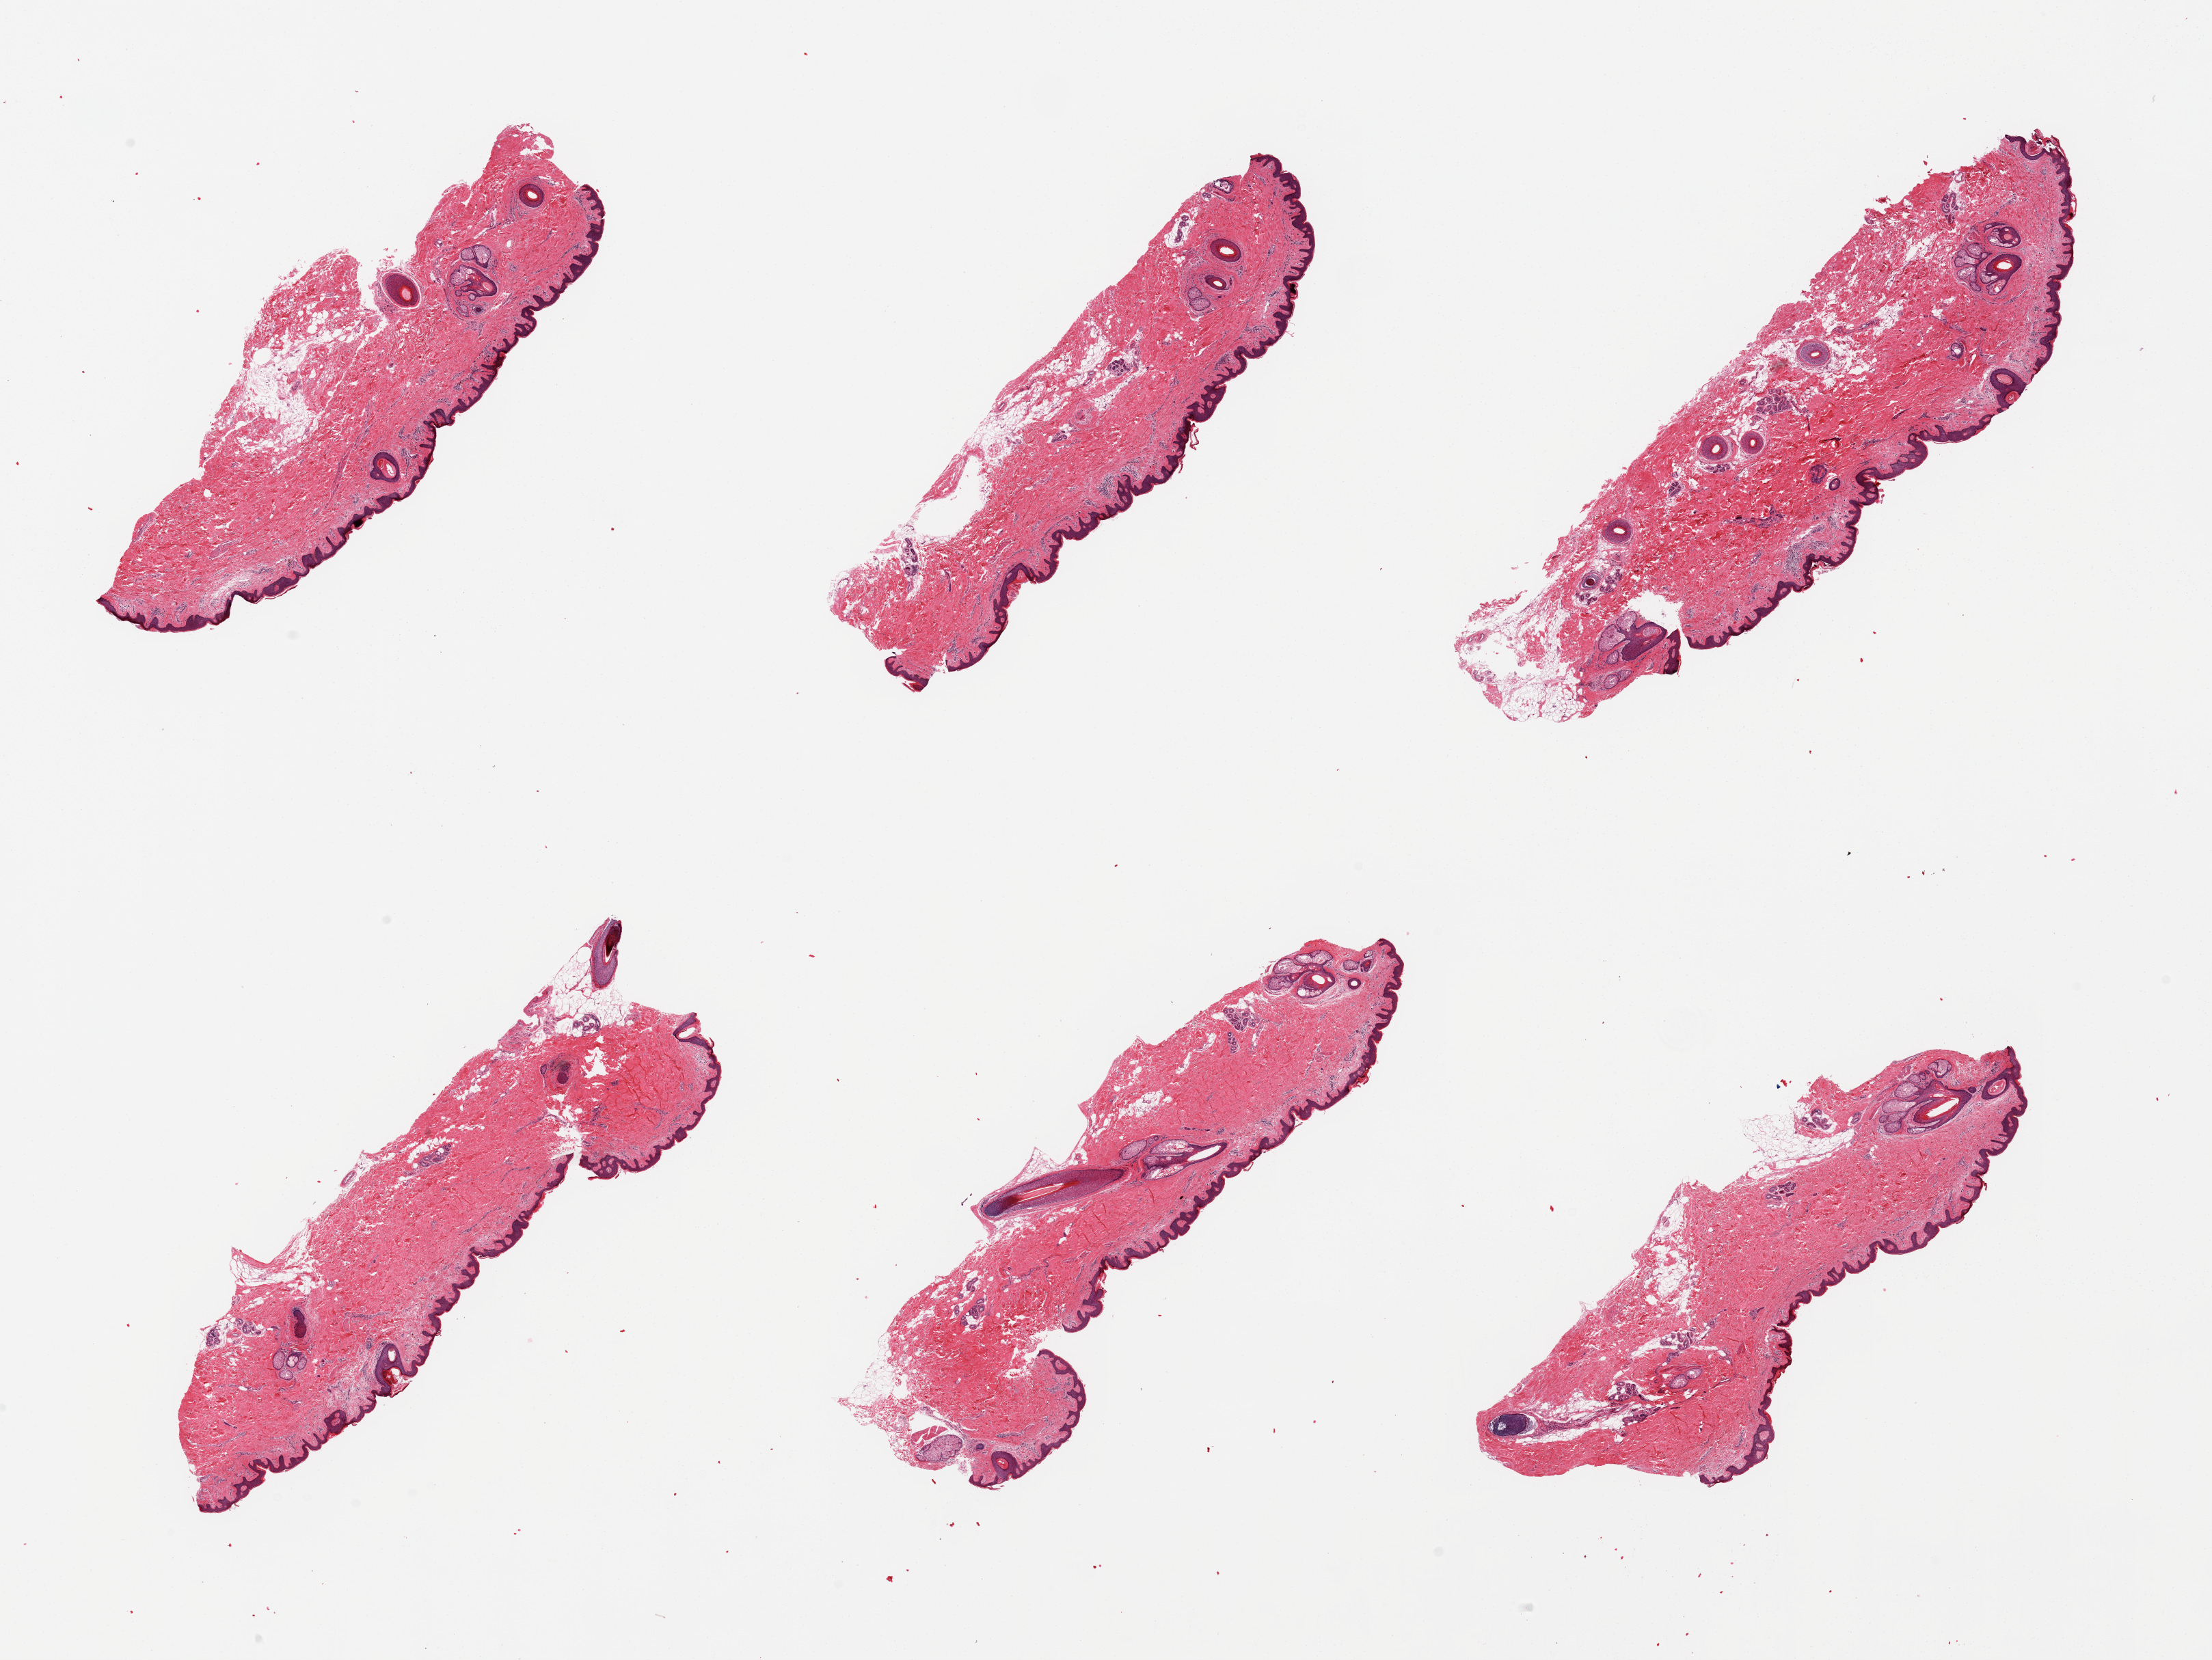
Whole-slide image, hematoxylin and eosin (H&E) stain, brightfield — a low-resolution overview of the entire scanned area, about 25.6 x 19.2 mm; PAXgene-fixed paraffin-embedded (PFPE) section; sampled site (target tissue): skin of suprapubic region; donor tissue sample. Donor sex: male.
Review note (as recorded): 6 pieces, no dermal fat, squamou epithelium is ~50 Microns.